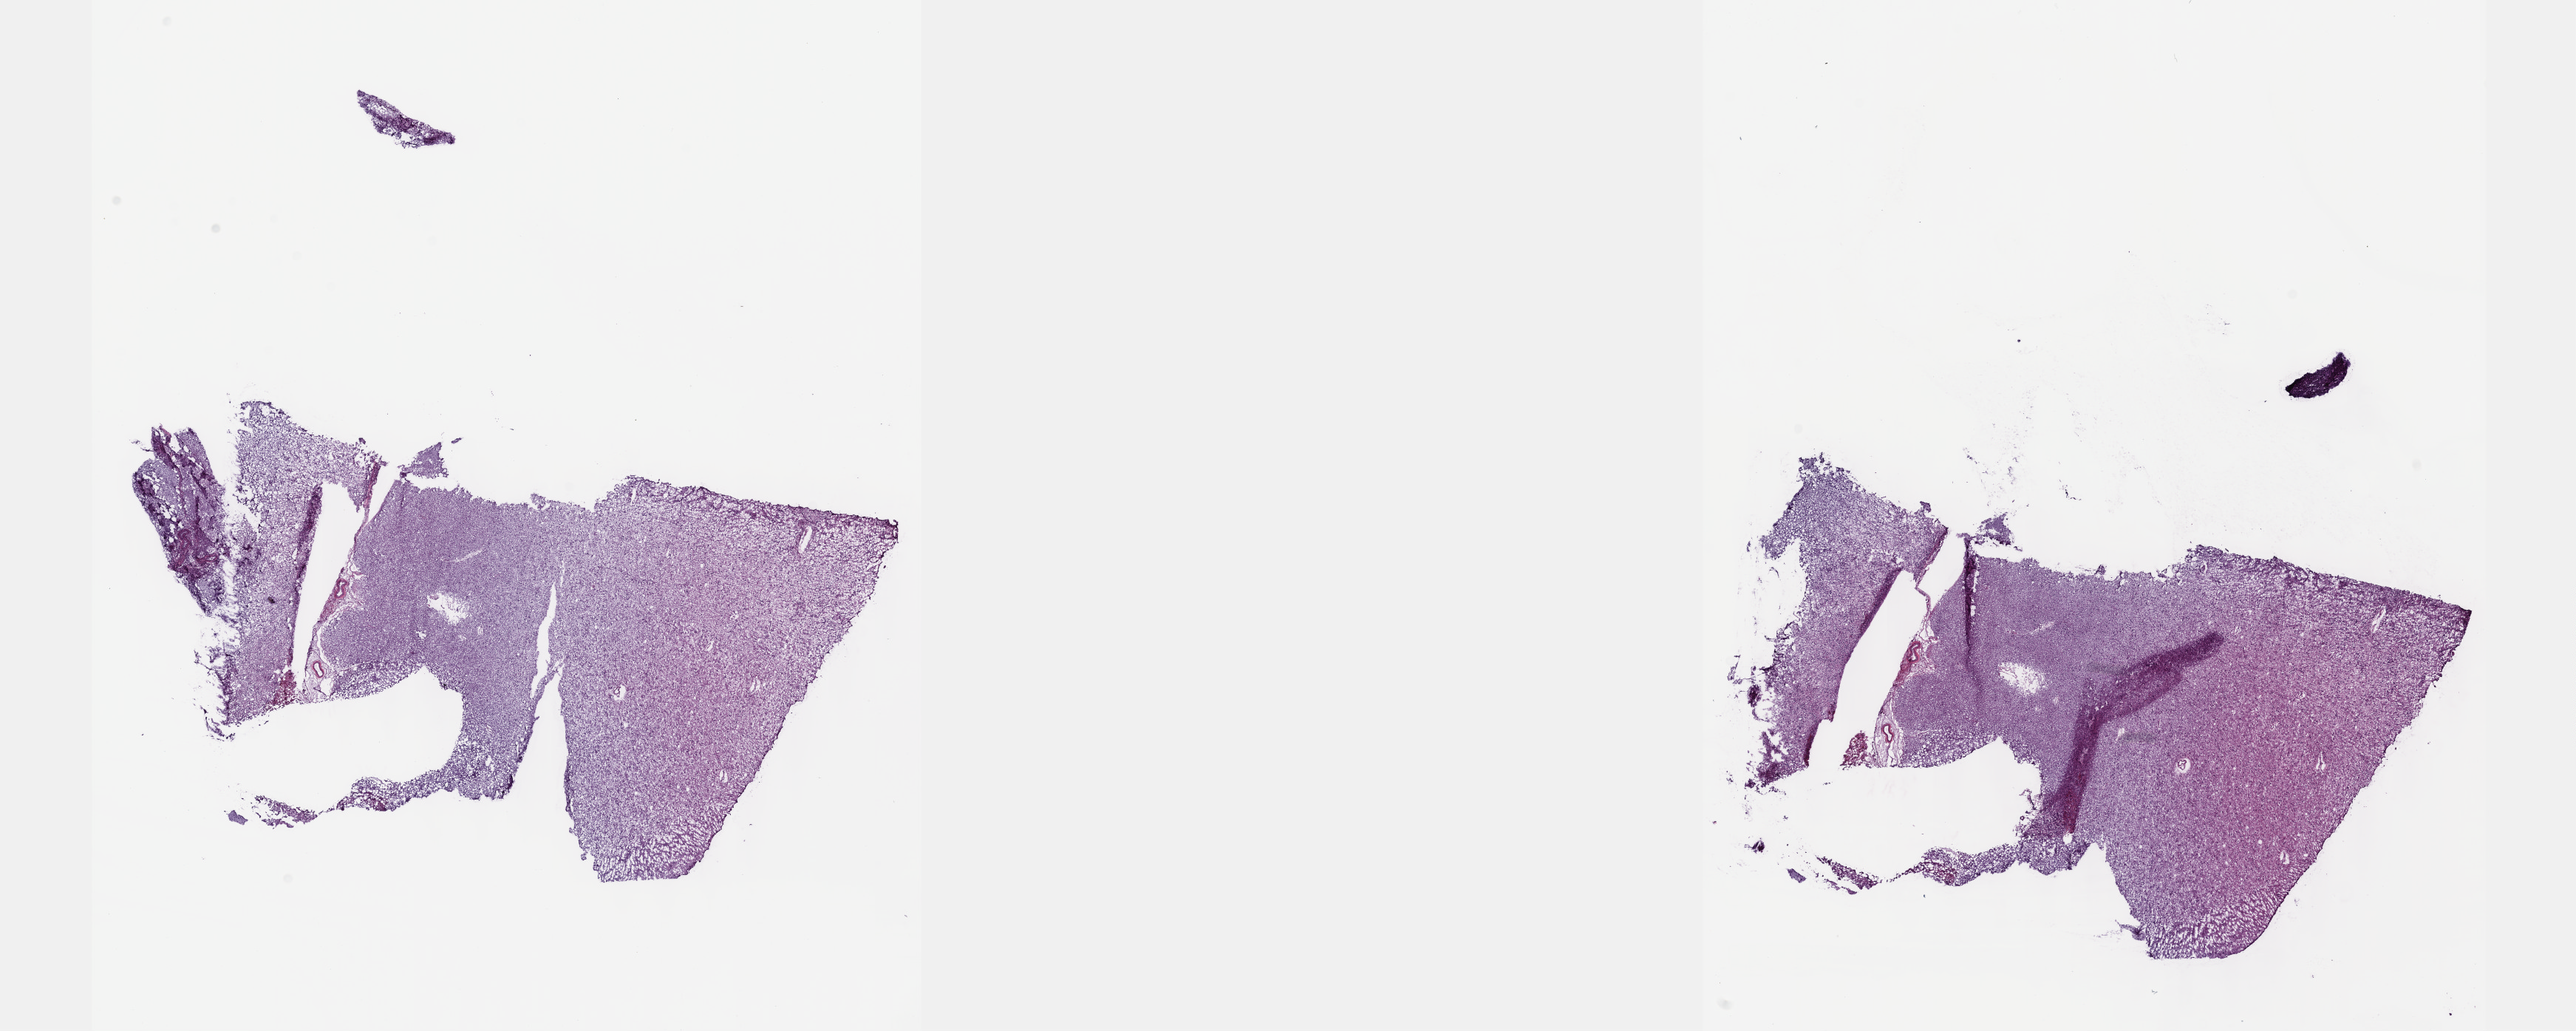
Digitized H&E tissue section (whole slide) — low-resolution overview of the scanned area, about 28.2 x 11.3 mm (slide scanned at 40x), frozen section, sample: primary tumour, brain. Patient: male, age at initial diagnosis 30 years. Histologic grade: G3 (poorly differentiated). Slide review estimates, as recorded: tumour cells 45%, tumour nuclei 75%, normal cells 10%, stromal cells 45%, necrosis 0%. Inflammatory infiltration, as recorded: lymphocyte infiltration 0%, monocyte infiltration 0%, neutrophil infiltration 0%.
- laterality: left
- histologic diagnosis: Astrocytoma, anaplastic (cerebrum)